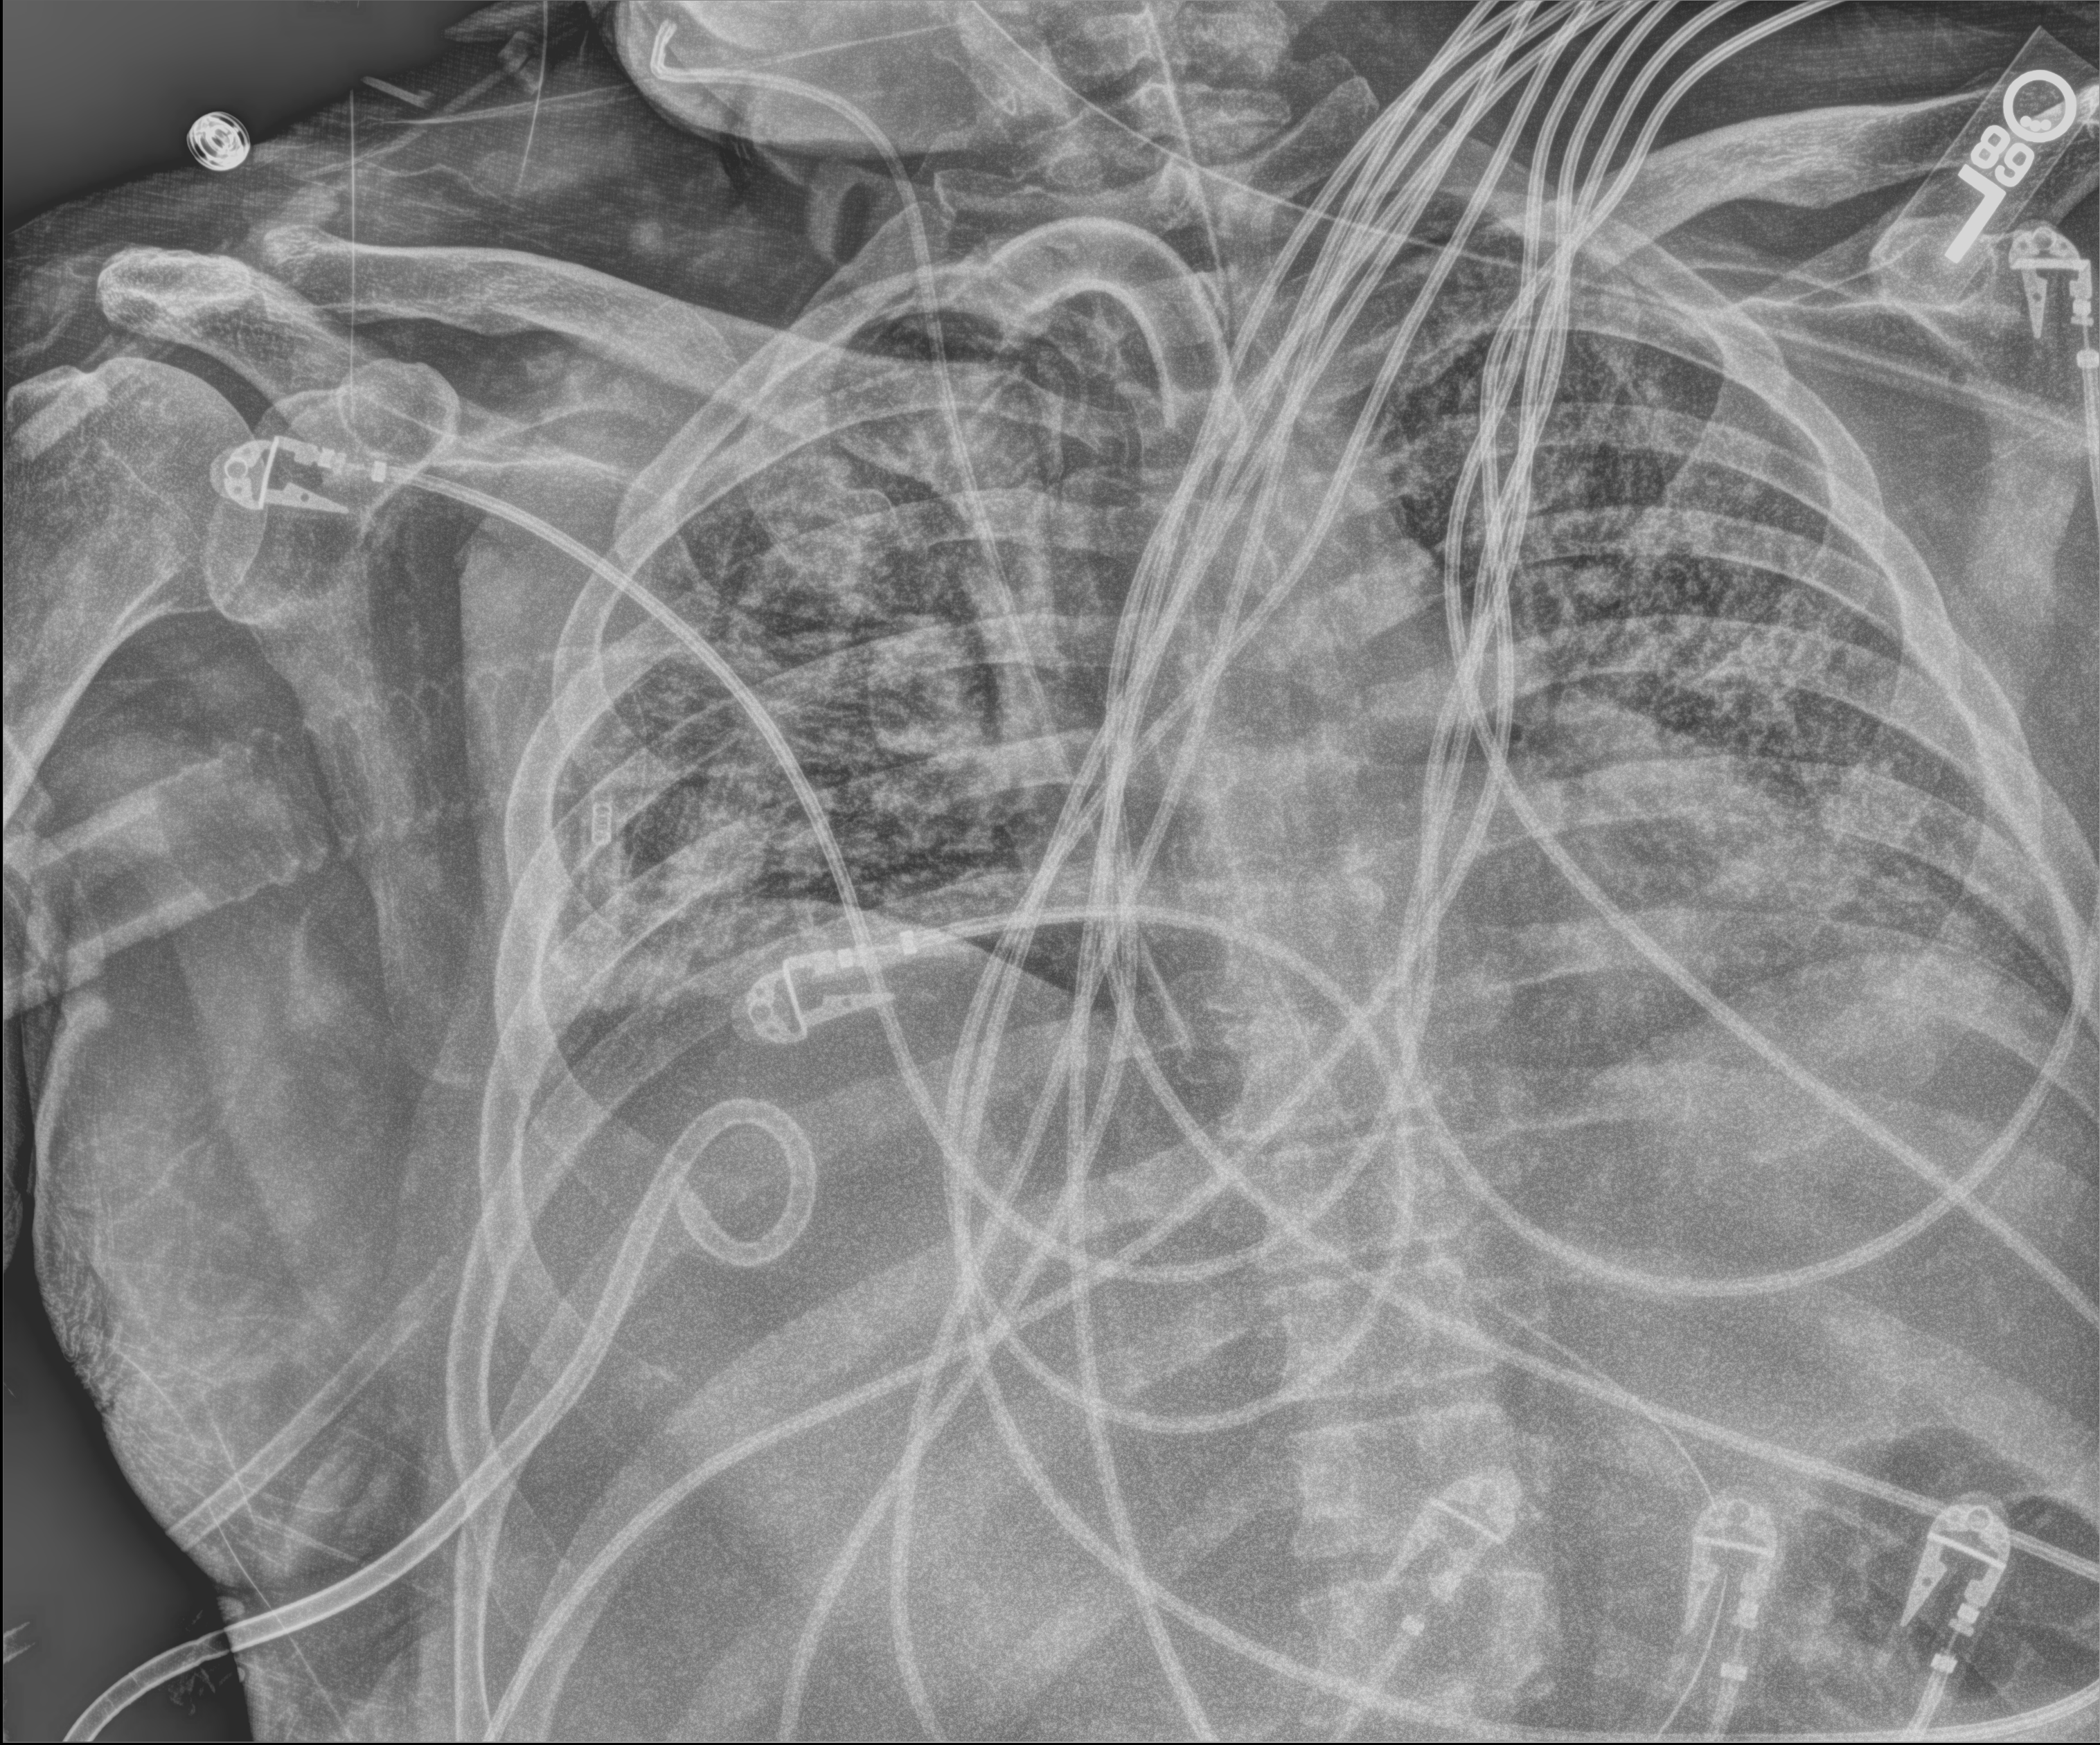
Chest X-ray (portable). Patient hospitalised with COVID-19; male, aged 18–59 years.
From the hospital-stay record, not from the radiograph (when in the stay this image was taken is not recorded):
- admitted to intensive care during this hospital stay: yes